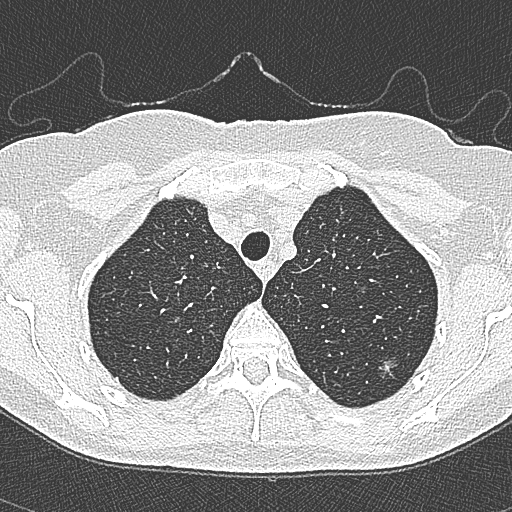
Chest CT (low-dose screening protocol), one axial image, second annual screen, lung window (W 1500 / L -600 HU), 1 mm slice thickness, lung (sharp) reconstruction kernel (B80f), 120 kVp, 512 × 512 image matrix, field of view 298 × 298 mm. Female, age 65 years at enrolment. Current smoker at enrolment.
• Expert-annotated lung lesion, bounding box (x1, y1, x2, y2) in pixels: (366, 349, 407, 386).
• The screening reader recorded 4 non-calcified nodules or masses ≥4 mm on this exam; which of them this box marks is not recorded.
• Official screen result: positive, change unspecified: nodule(s) >= 4 mm or enlarging nodule(s), mass(es), or other non-specific abnormalities suspicious for lung cancer.
• Lung cancer was diagnosed 54 days after this screen: bronchiolo-alveolar carcinoma, non-mucinous, left upper lobe, stage IA (AJCC 6th edition), 10 mm at pathology.